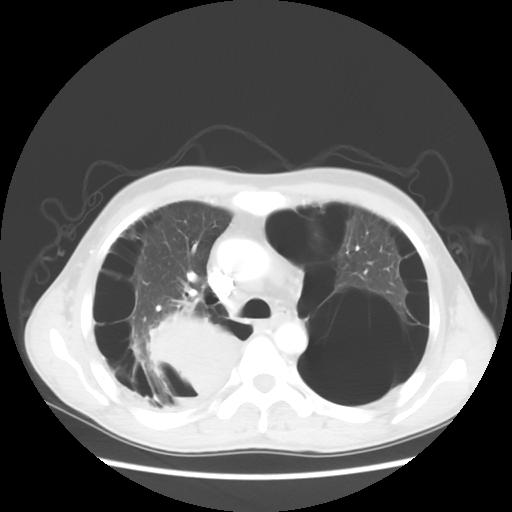
Chest CT, one axial slice; position 37 of 56 along the scan axis; reconstruction kernel STANDARD; 140 kVp; lung window (W 1500 / L -600 HU); 5 mm slice thickness; 512 × 512 image matrix, field of view 351 × 351 mm. Male patient, age 41 years. From the clinical record (not read from this slice): clinical TNM (as recorded): T4 N0 M1a.
Outlined on this slice (rectangle marked by the reading radiologist):
- lung tumour (recorded histology: large cell carcinoma): bounding box [x1, y1, x2, y2] px = [145, 309, 239, 400]